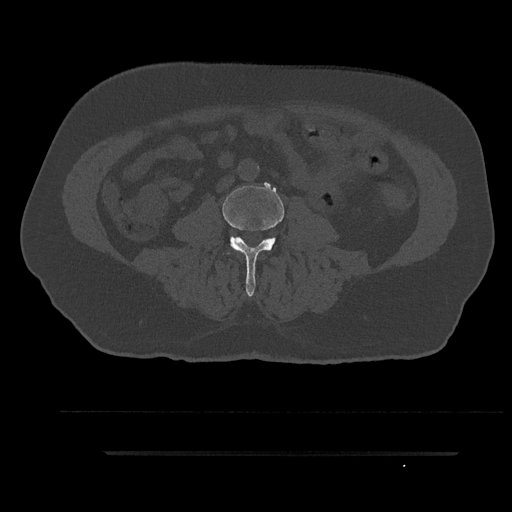
CT including the spine, one axial slice. Slice 30 of 797 in the series (ordered by position). Reconstruction kernel Br40s/3. Bone window (W 1800 / L 400 HU). 0.5 mm slice thickness. 512 × 512 image matrix, field of view 432 × 432 mm. Patient: male, 63 years. Case-level facts recorded for this patient, not image findings: primary cancer: renal.
Structures marked on this image (semi-automatically segmented with operator editing):
- L3 vertebra: bounding box <222,185,284,297> (left, top, right, bottom; pixels)
- L4 vertebra: <268,238,273,246>